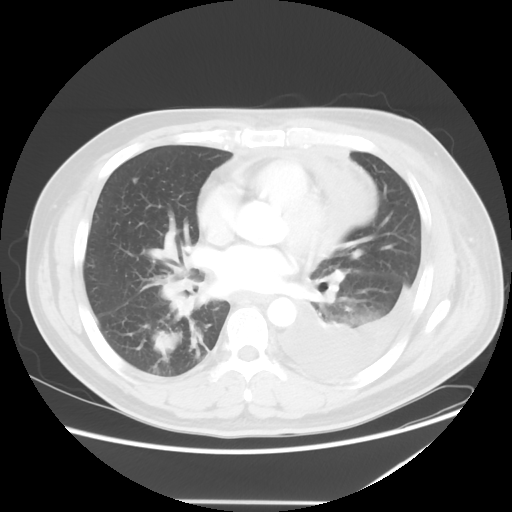
Chest CT, one axial slice; position 24 of 52 along the scan axis; reconstruction kernel STANDARD; 120 kVp; lung window (W 1500 / L -600 HU); 5 mm slice thickness; 512 × 512 image matrix. Patient: male, 42 years. Case-level facts recorded for this patient, not image findings: clinical TNM (as recorded): T2 N1 M1.
Structures marked on this image (rectangle marked by the reading radiologist):
- lung tumour (recorded histology: adenocarcinoma): bounding box <152,323,189,362> (left, top, right, bottom; pixels)